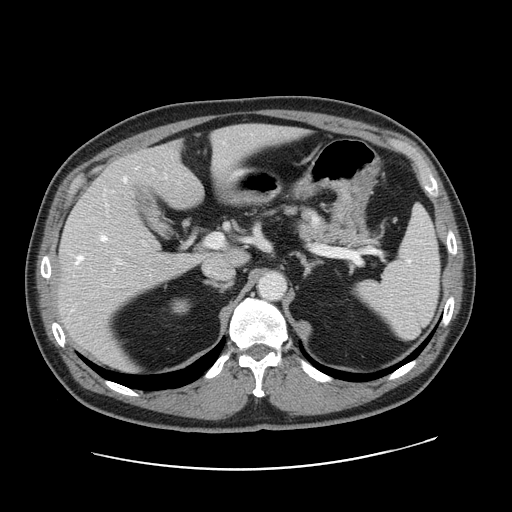
Contrast-enhanced abdominal CT, one axial slice. Slice 100 of 178 in the series (ordered by position). 120 kVp. Intravenous contrast given. Soft-tissue window (W 400 / L 40 HU). 2.5 mm slice thickness. 512 × 512 image matrix, field of view 403 × 403 mm. Male patient, age 63 years. From the clinical record (not read from this slice): diagnosis: colorectal cancer liver metastases, imaged before liver resection; multiple liver metastases: yes; largest metastasis: 8 cm; chemotherapy before resection: no.
Structures marked on this image (expert manual segmentation):
- hepatic veins: box from (x=77, y=177) to (x=127, y=270) px
- liver: (x=58, y=125)–(x=293, y=366)
- planned liver remnant (the part of the liver to remain after resection): (x=120, y=125)–(x=294, y=262)
- portal vein (with intrahepatic branches): (x=116, y=234)–(x=224, y=262)